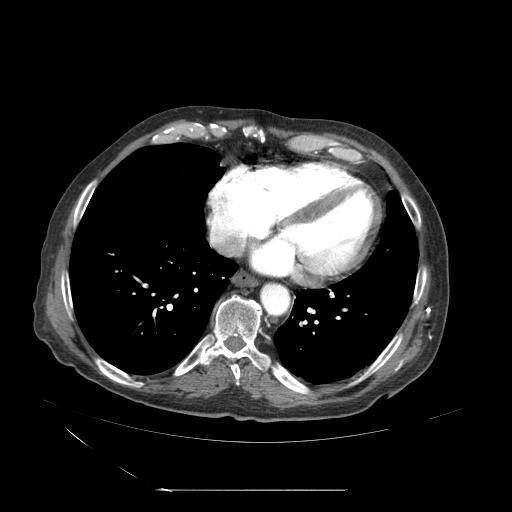
Contrast-enhanced abdominal CT (liver protocol), one axial slice. Slice 64 of 71 in the series (ordered by position). 120 kVp. Soft-tissue window (W 400 / L 40 HU). 2.5 mm slice thickness. 512 × 512 image matrix, field of view 440 × 440 mm. Case-level facts recorded for this patient, not image findings: diagnosis: hepatocellular carcinoma (patient treated with transarterial chemoembolisation; whether this scan precedes or follows treatment is not stated here); TNM stage (as recorded): Stage-II; Child-Pugh class: A; tumour nodularity: multinodular.
Annotated regions visible in this slice (semi-automatically segmented with operator editing):
- abdominal aorta: bounding box <260,282,289,316> (left, top, right, bottom; pixels)